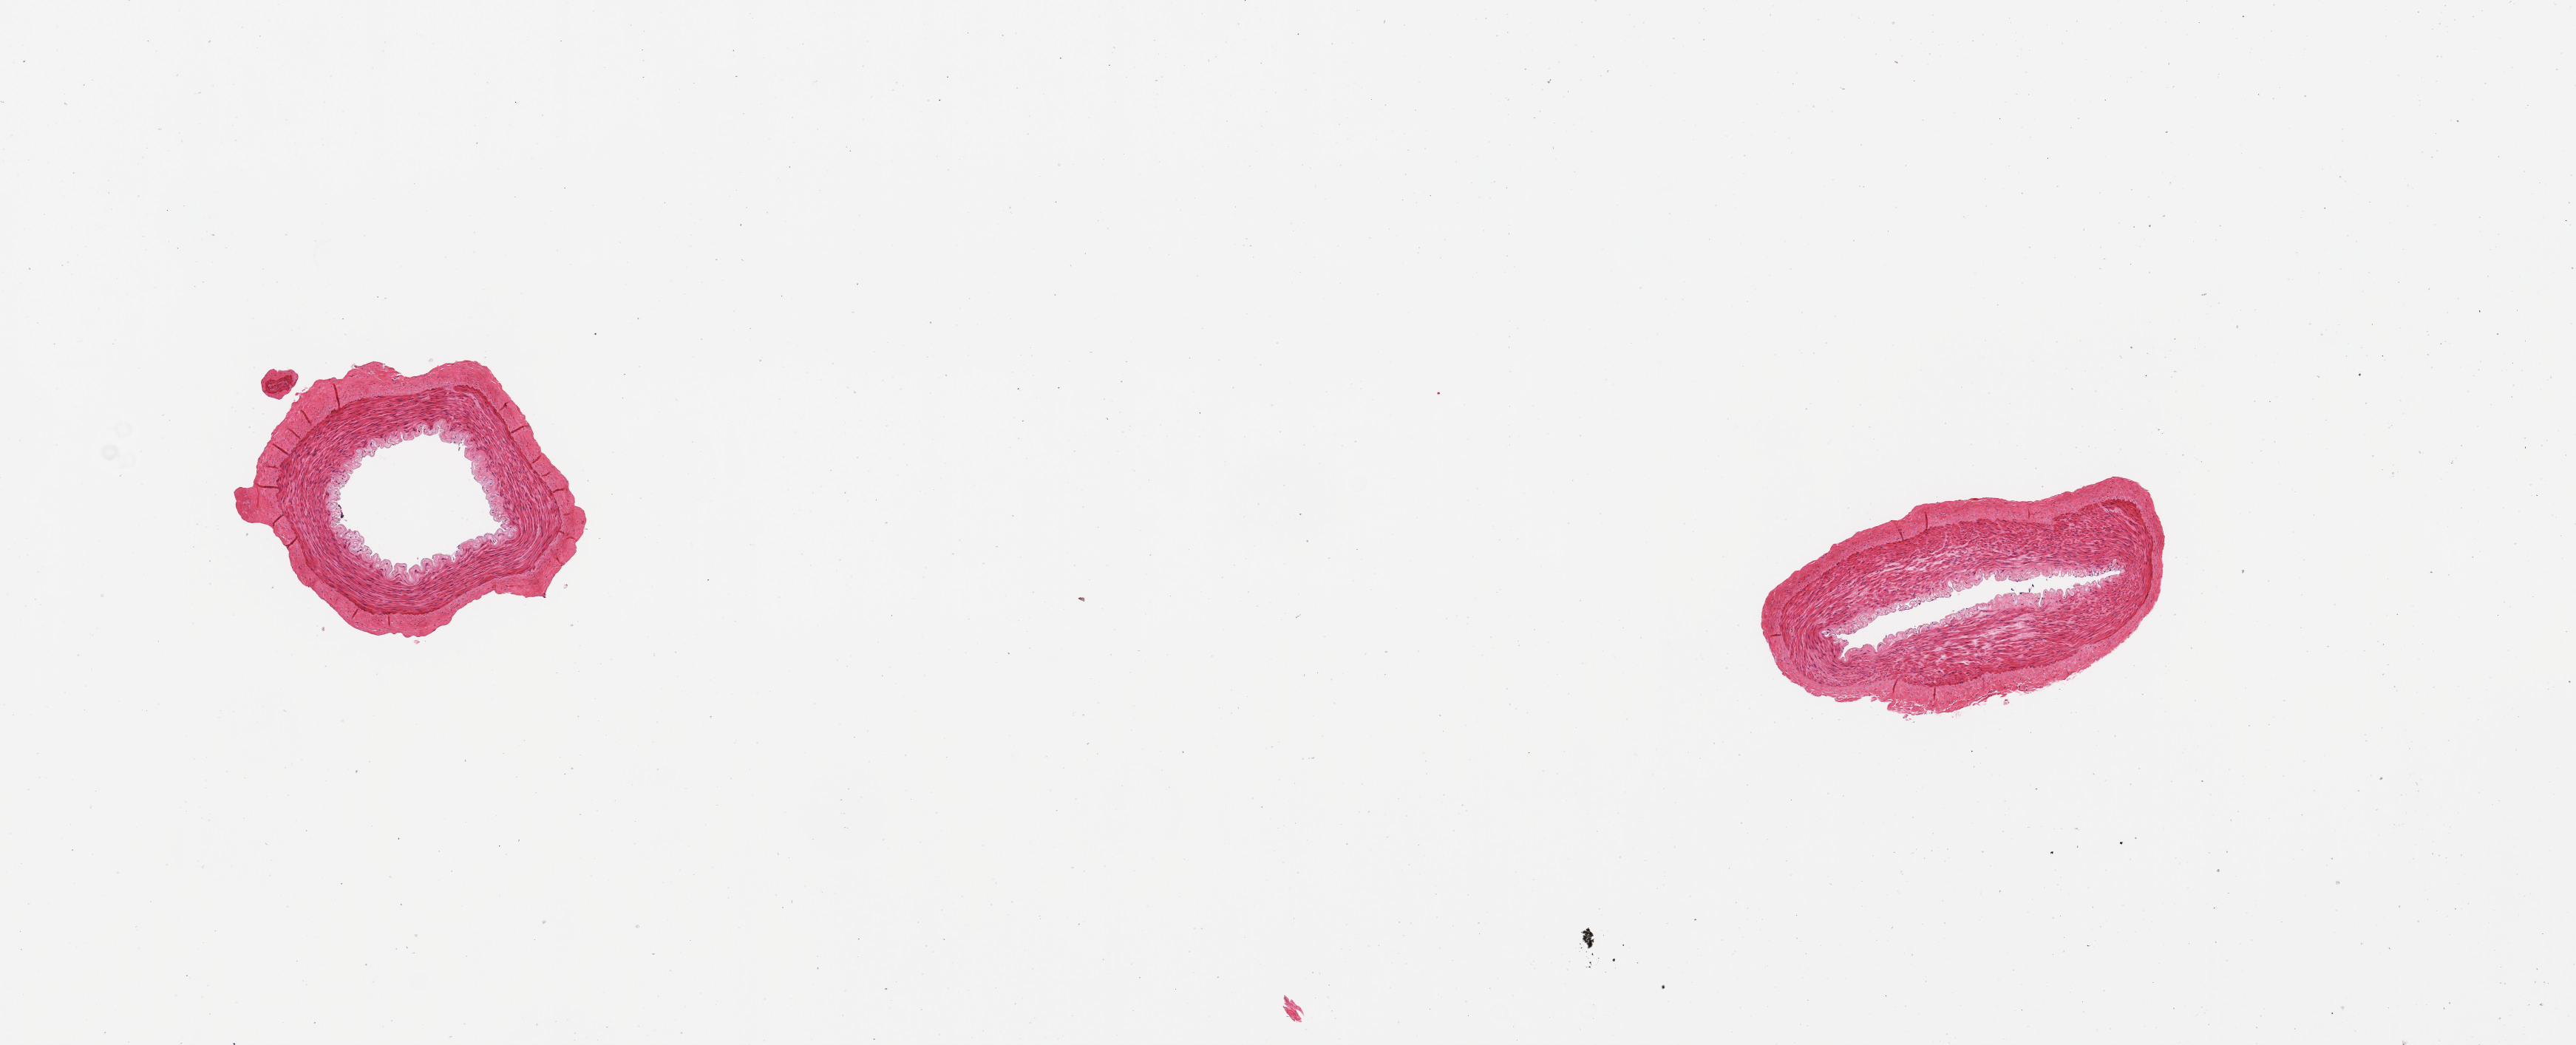
Whole-slide image, haematoxylin and eosin stain, low-resolution overview of the scanned area, about 13.8 x 5.6 mm (acquisition: 20x scan); PAXgene-fixed paraffin-embedded (PFPE) section; section of tibial artery (target tissue); tissue donor sample. Donor sex: female.
Reviewer comment on this tissue sample: 2 pieces; well trimmed.